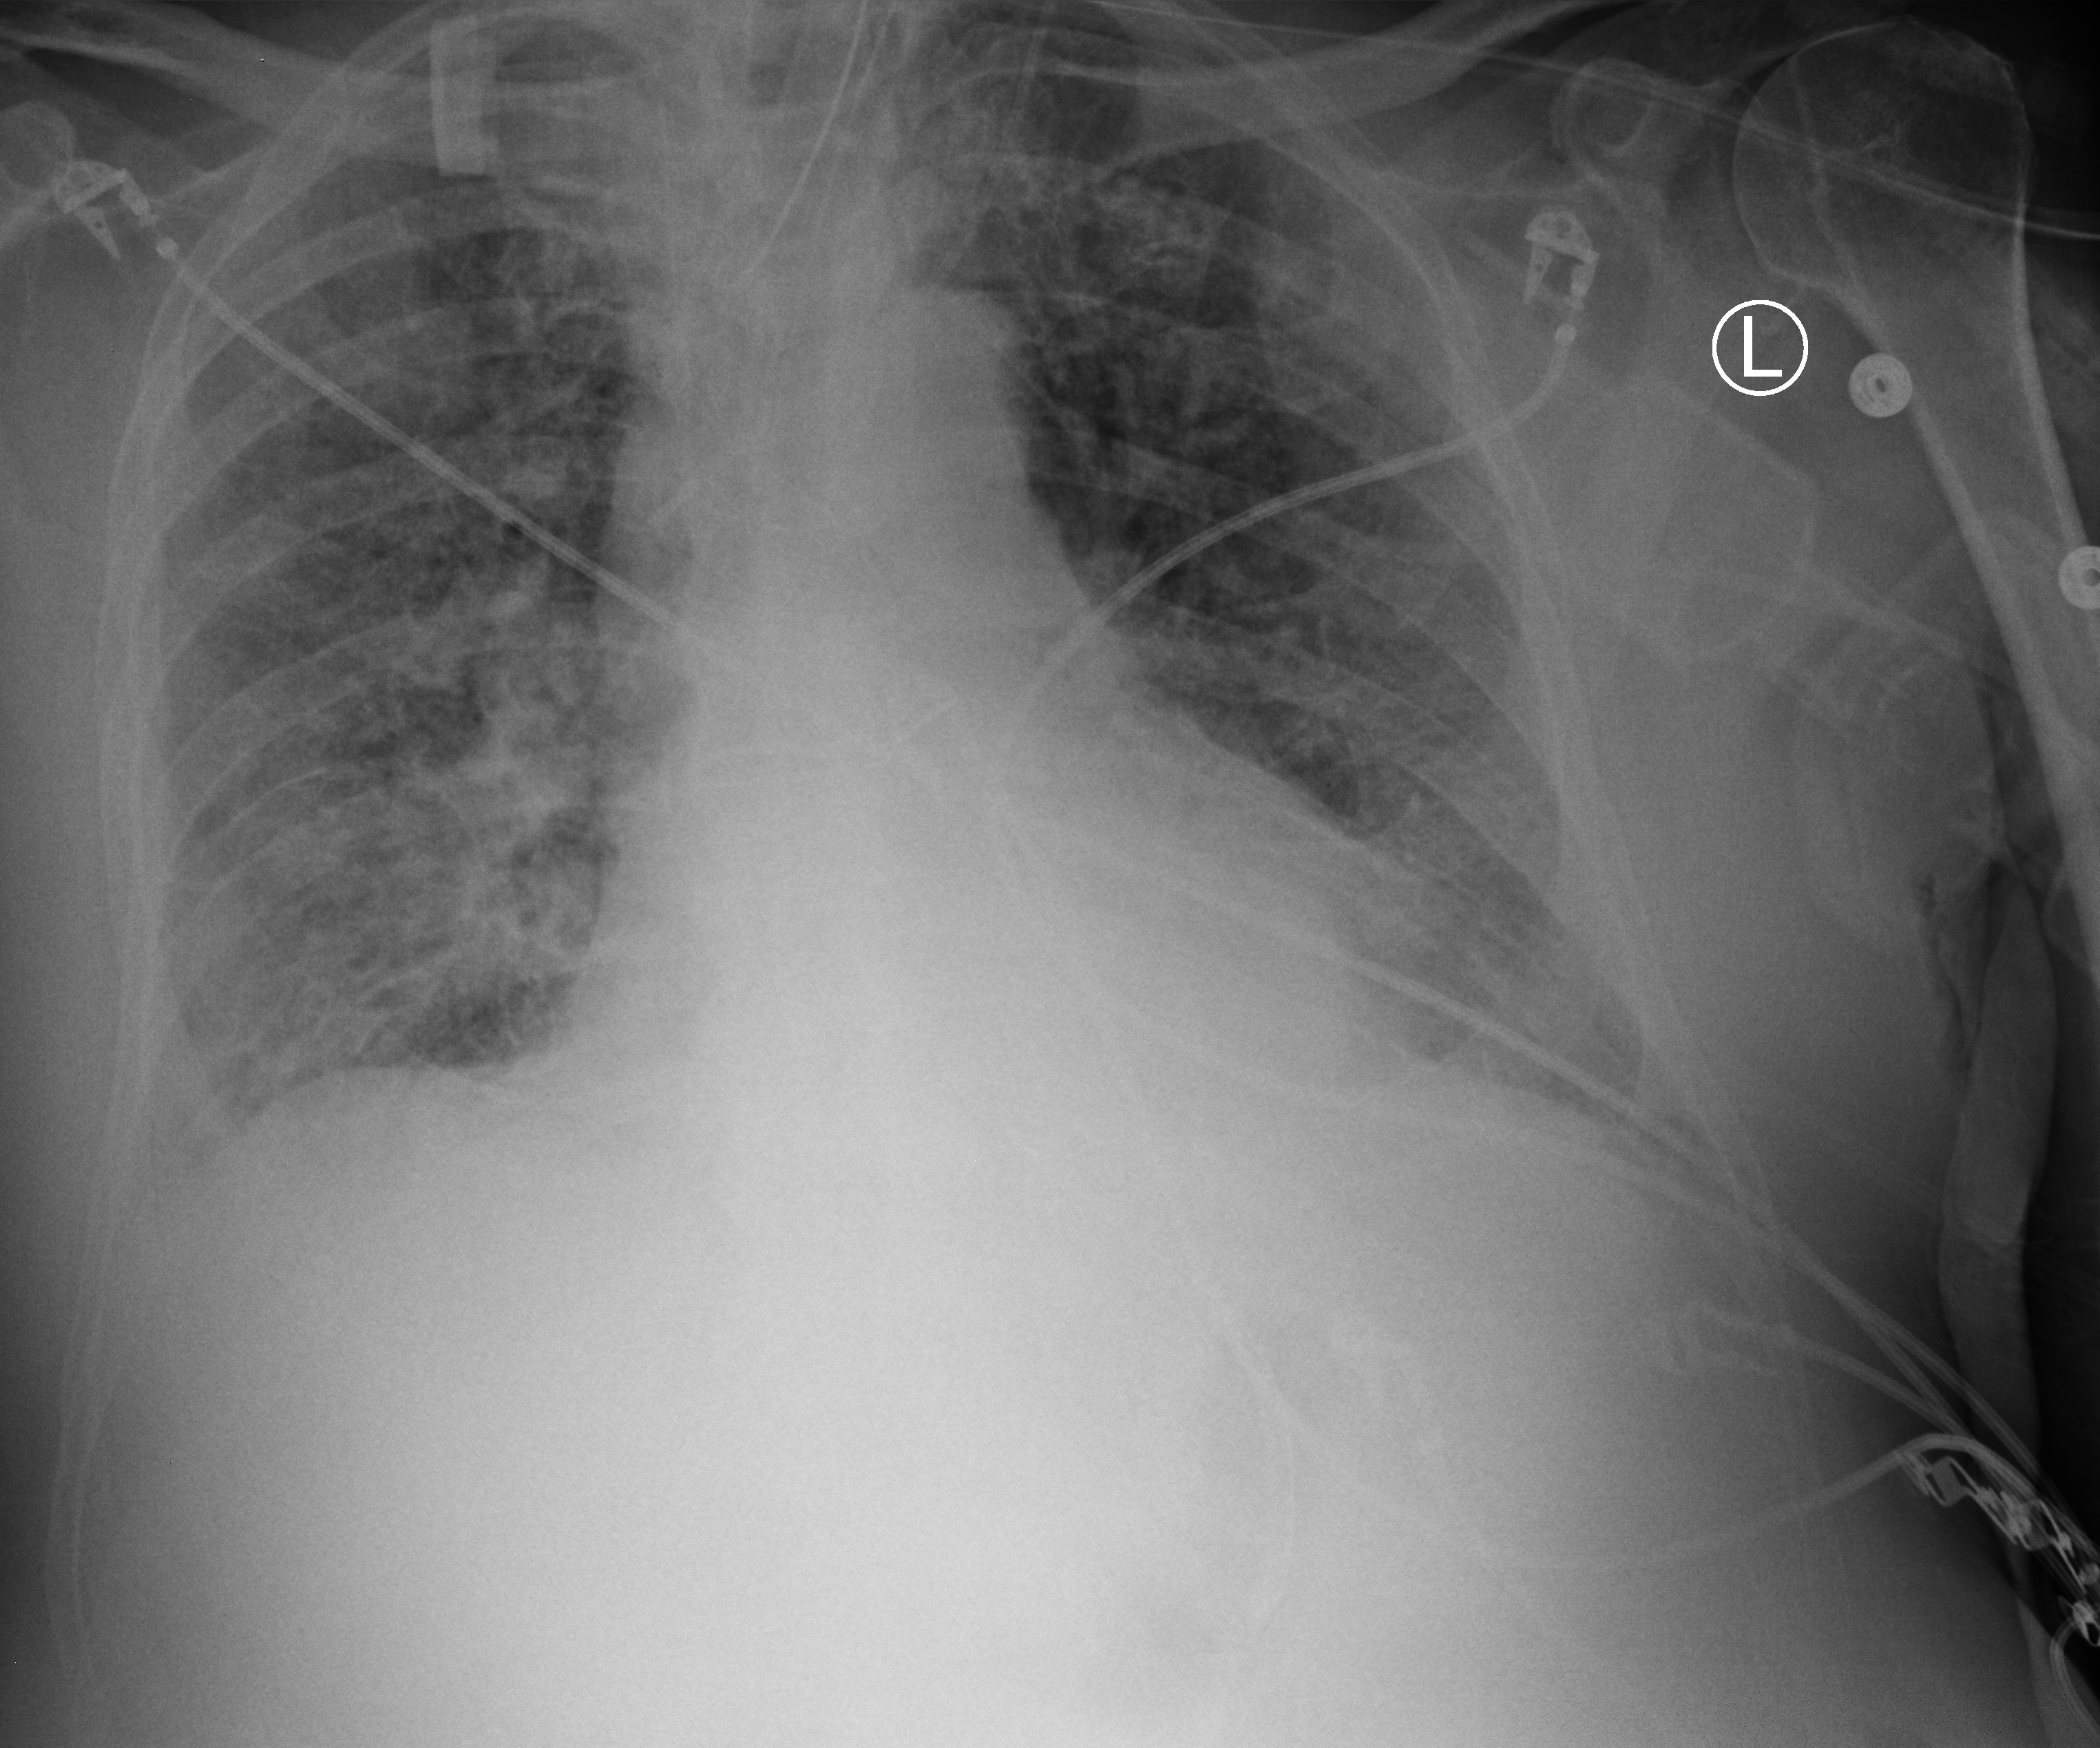
Chest X-ray (portable), anteroposterior (AP) projection. Patient hospitalised with COVID-19; male, aged 75–90 years.
From the hospital-stay record, not from the radiograph (when in the stay this image was taken is not recorded): admitted to intensive care during this hospital stay: yes; COPD (admission record): no; mechanically ventilated during this hospital stay: yes.